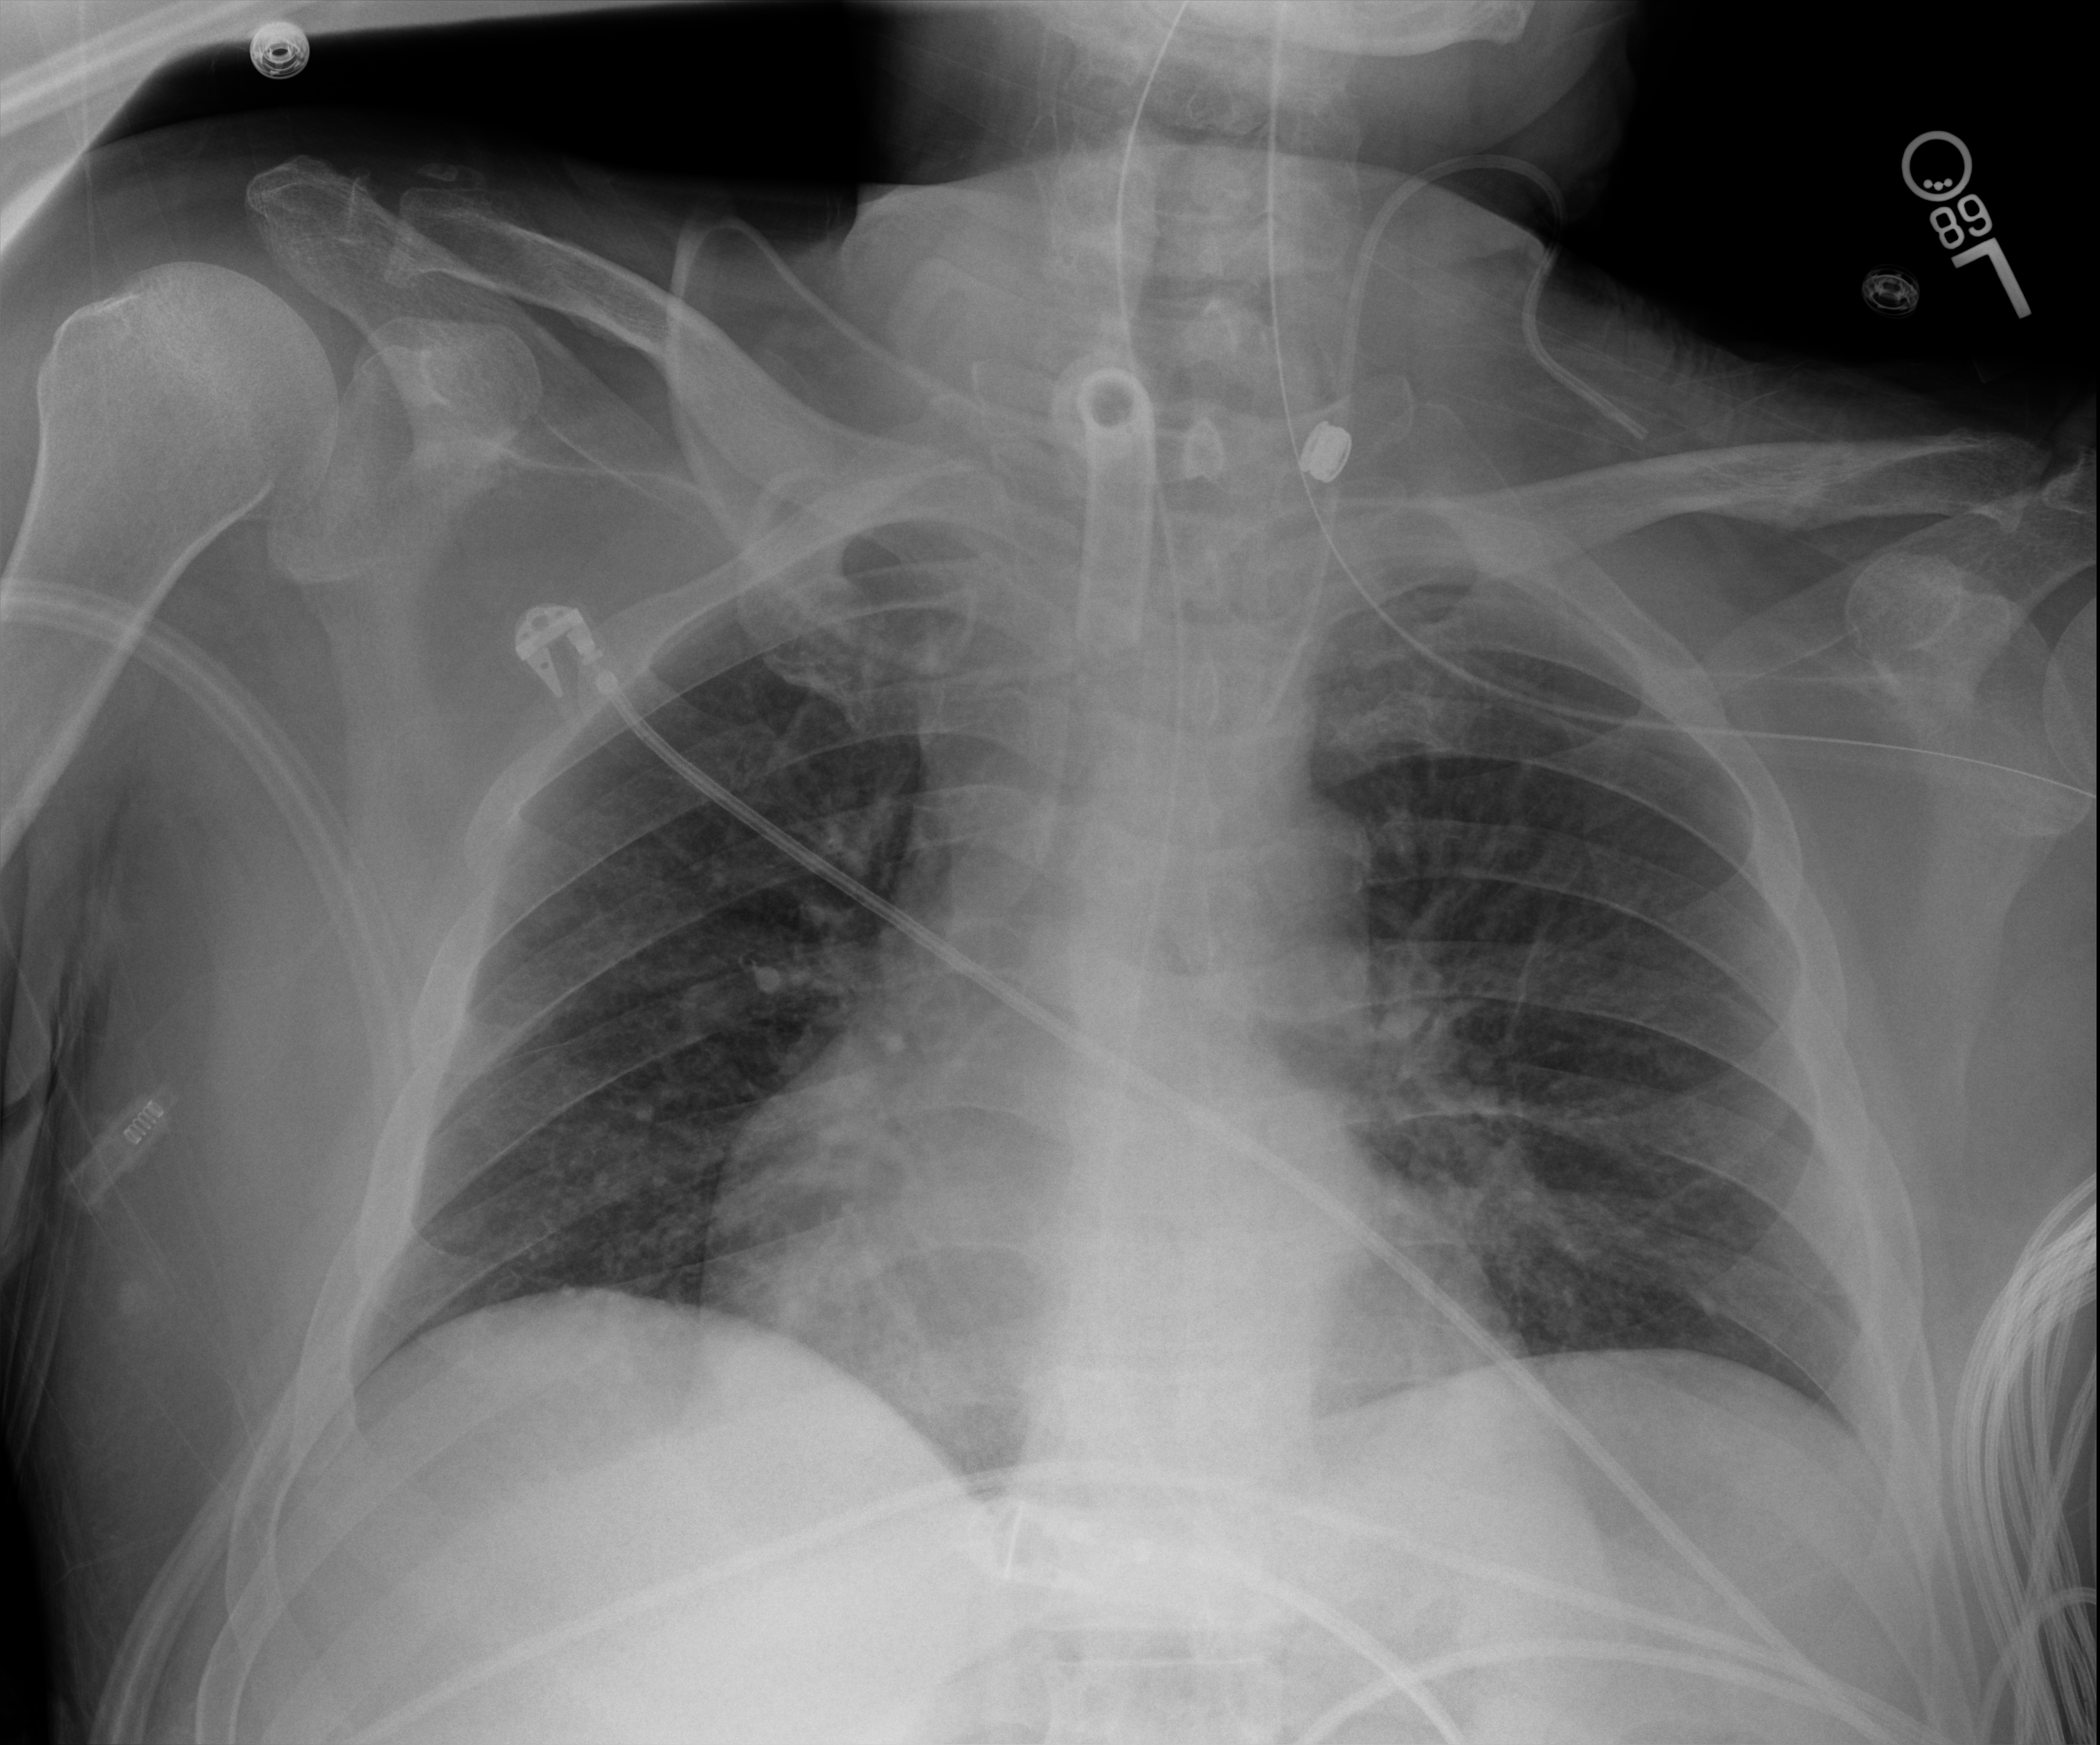
Bedside chest radiograph (digital radiography), anteroposterior (AP) projection. Patient hospitalised with COVID-19; male, aged 18–59 years.
From the hospital-stay record, not from the radiograph (when in the stay this image was taken is not recorded):
- length of hospital stay: 65 days
- mechanically ventilated during this hospital stay: yes